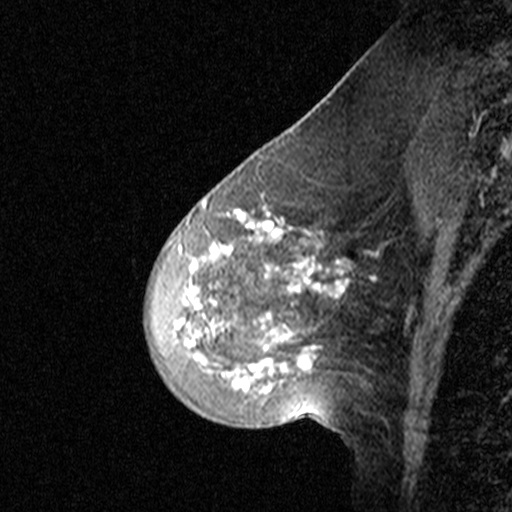
Breast MRI (dynamic contrast-enhanced), one sagittal slice; slice 15 of 44 in the series (ordered by position); dynamic contrast-enhanced study with each time point stored as its own series, time point 2 of 3 at this slice position (early post-contrast, ordered by acquisition time); 1.5 T; TE 4.5 ms, TR 11 ms; 3 mm slice thickness; 512 × 512 image matrix, field of view 200 × 200 mm. Female patient, age 46 years. From the clinical record (not read from this slice): setting: breast cancer imaged before/during neoadjuvant chemotherapy; receptor status: HER2-positive.
Annotated regions visible in this slice (semi-automatically segmented with operator editing):
- analysis volume of interest (the breast-tissue region the enhancement analysis was run in; not a lesion): bounding box (x1, y1, x2, y2) in pixels: (144, 172, 359, 393)
- tumour enhancement mask (voxels above the 90 % enhancement threshold inside the analysis volume of interest): (184, 198, 347, 381)